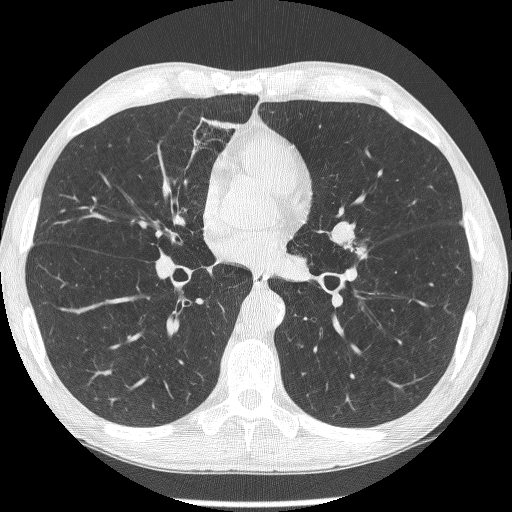
Axial slice from a low-dose chest CT screening exam, second annual screen, lung window (W 1500 / L -600 HU), 1.25 mm slice thickness, lung (sharp) reconstruction kernel (BONE), slice 134 of 293 in the series. Male, age 62 years at enrolment. Former smoker at enrolment.
Lesion marked by an expert reader, bounding box <321,217,370,265> (left, top, right, bottom; pixels). The screening reader recorded 2 non-calcified nodules or masses ≥4 mm on this exam (lingula, lingula); which of them this box marks is not recorded.